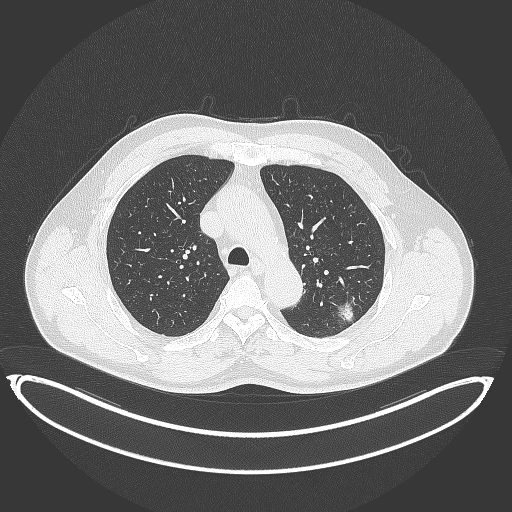
Chest CT, one axial slice; slice 260 of 399 in the series (ordered by position); reconstruction kernel B70f; 120 kVp; lung window (W 1500 / L -600 HU); 512 × 512 image matrix, field of view 469 × 469 mm. Patient: male, 58 years. Case-level facts recorded for this patient, not image findings: clinical TNM (as recorded): T1c N0 M0; histopathological grade: G1-2.
Annotated regions visible in this slice (bounding box drawn by a radiologist):
- lung tumour (recorded histology: adenocarcinoma): box from (x=333, y=301) to (x=362, y=329) px